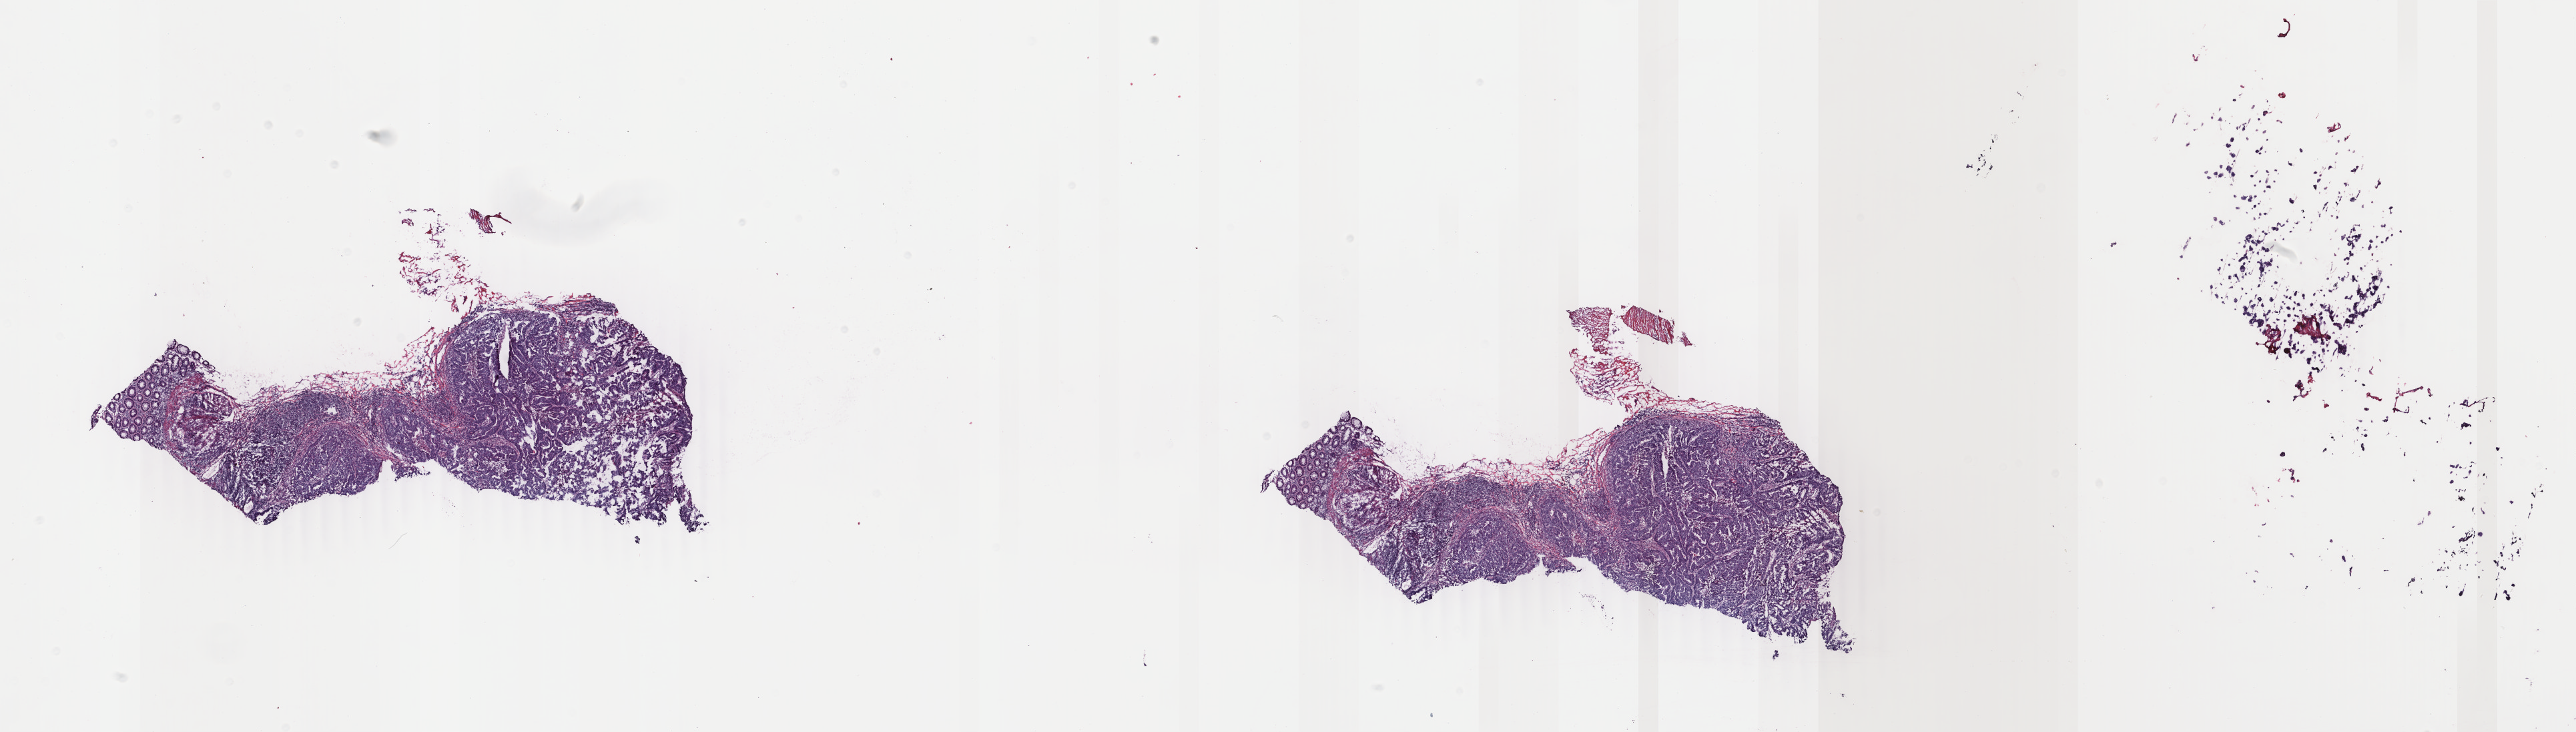
Hematoxylin and eosin (H&E) stained whole-slide image, shown as a low-resolution overview of the whole scanned area (about 30.7 x 8.7 mm); frozen section from the top of the tissue portion; primary tumour sample from the rectum. Patient: female, age at initial diagnosis 49 years. Composition of this section per pathologist review: tumour cells 75%, tumour nuclei 75%, normal cells 8%, stromal cells 17%, necrosis 0%. Inflammatory infiltration, as recorded: lymphocyte infiltration 5%, monocyte infiltration 0%, neutrophil infiltration 0%.
* TNM: T3 N0 M0
* AJCC pathologic stage: II
* lymph nodes positive (case pathology): 0 of 17 examined
* histologic diagnosis: Adenocarcinoma, NOS